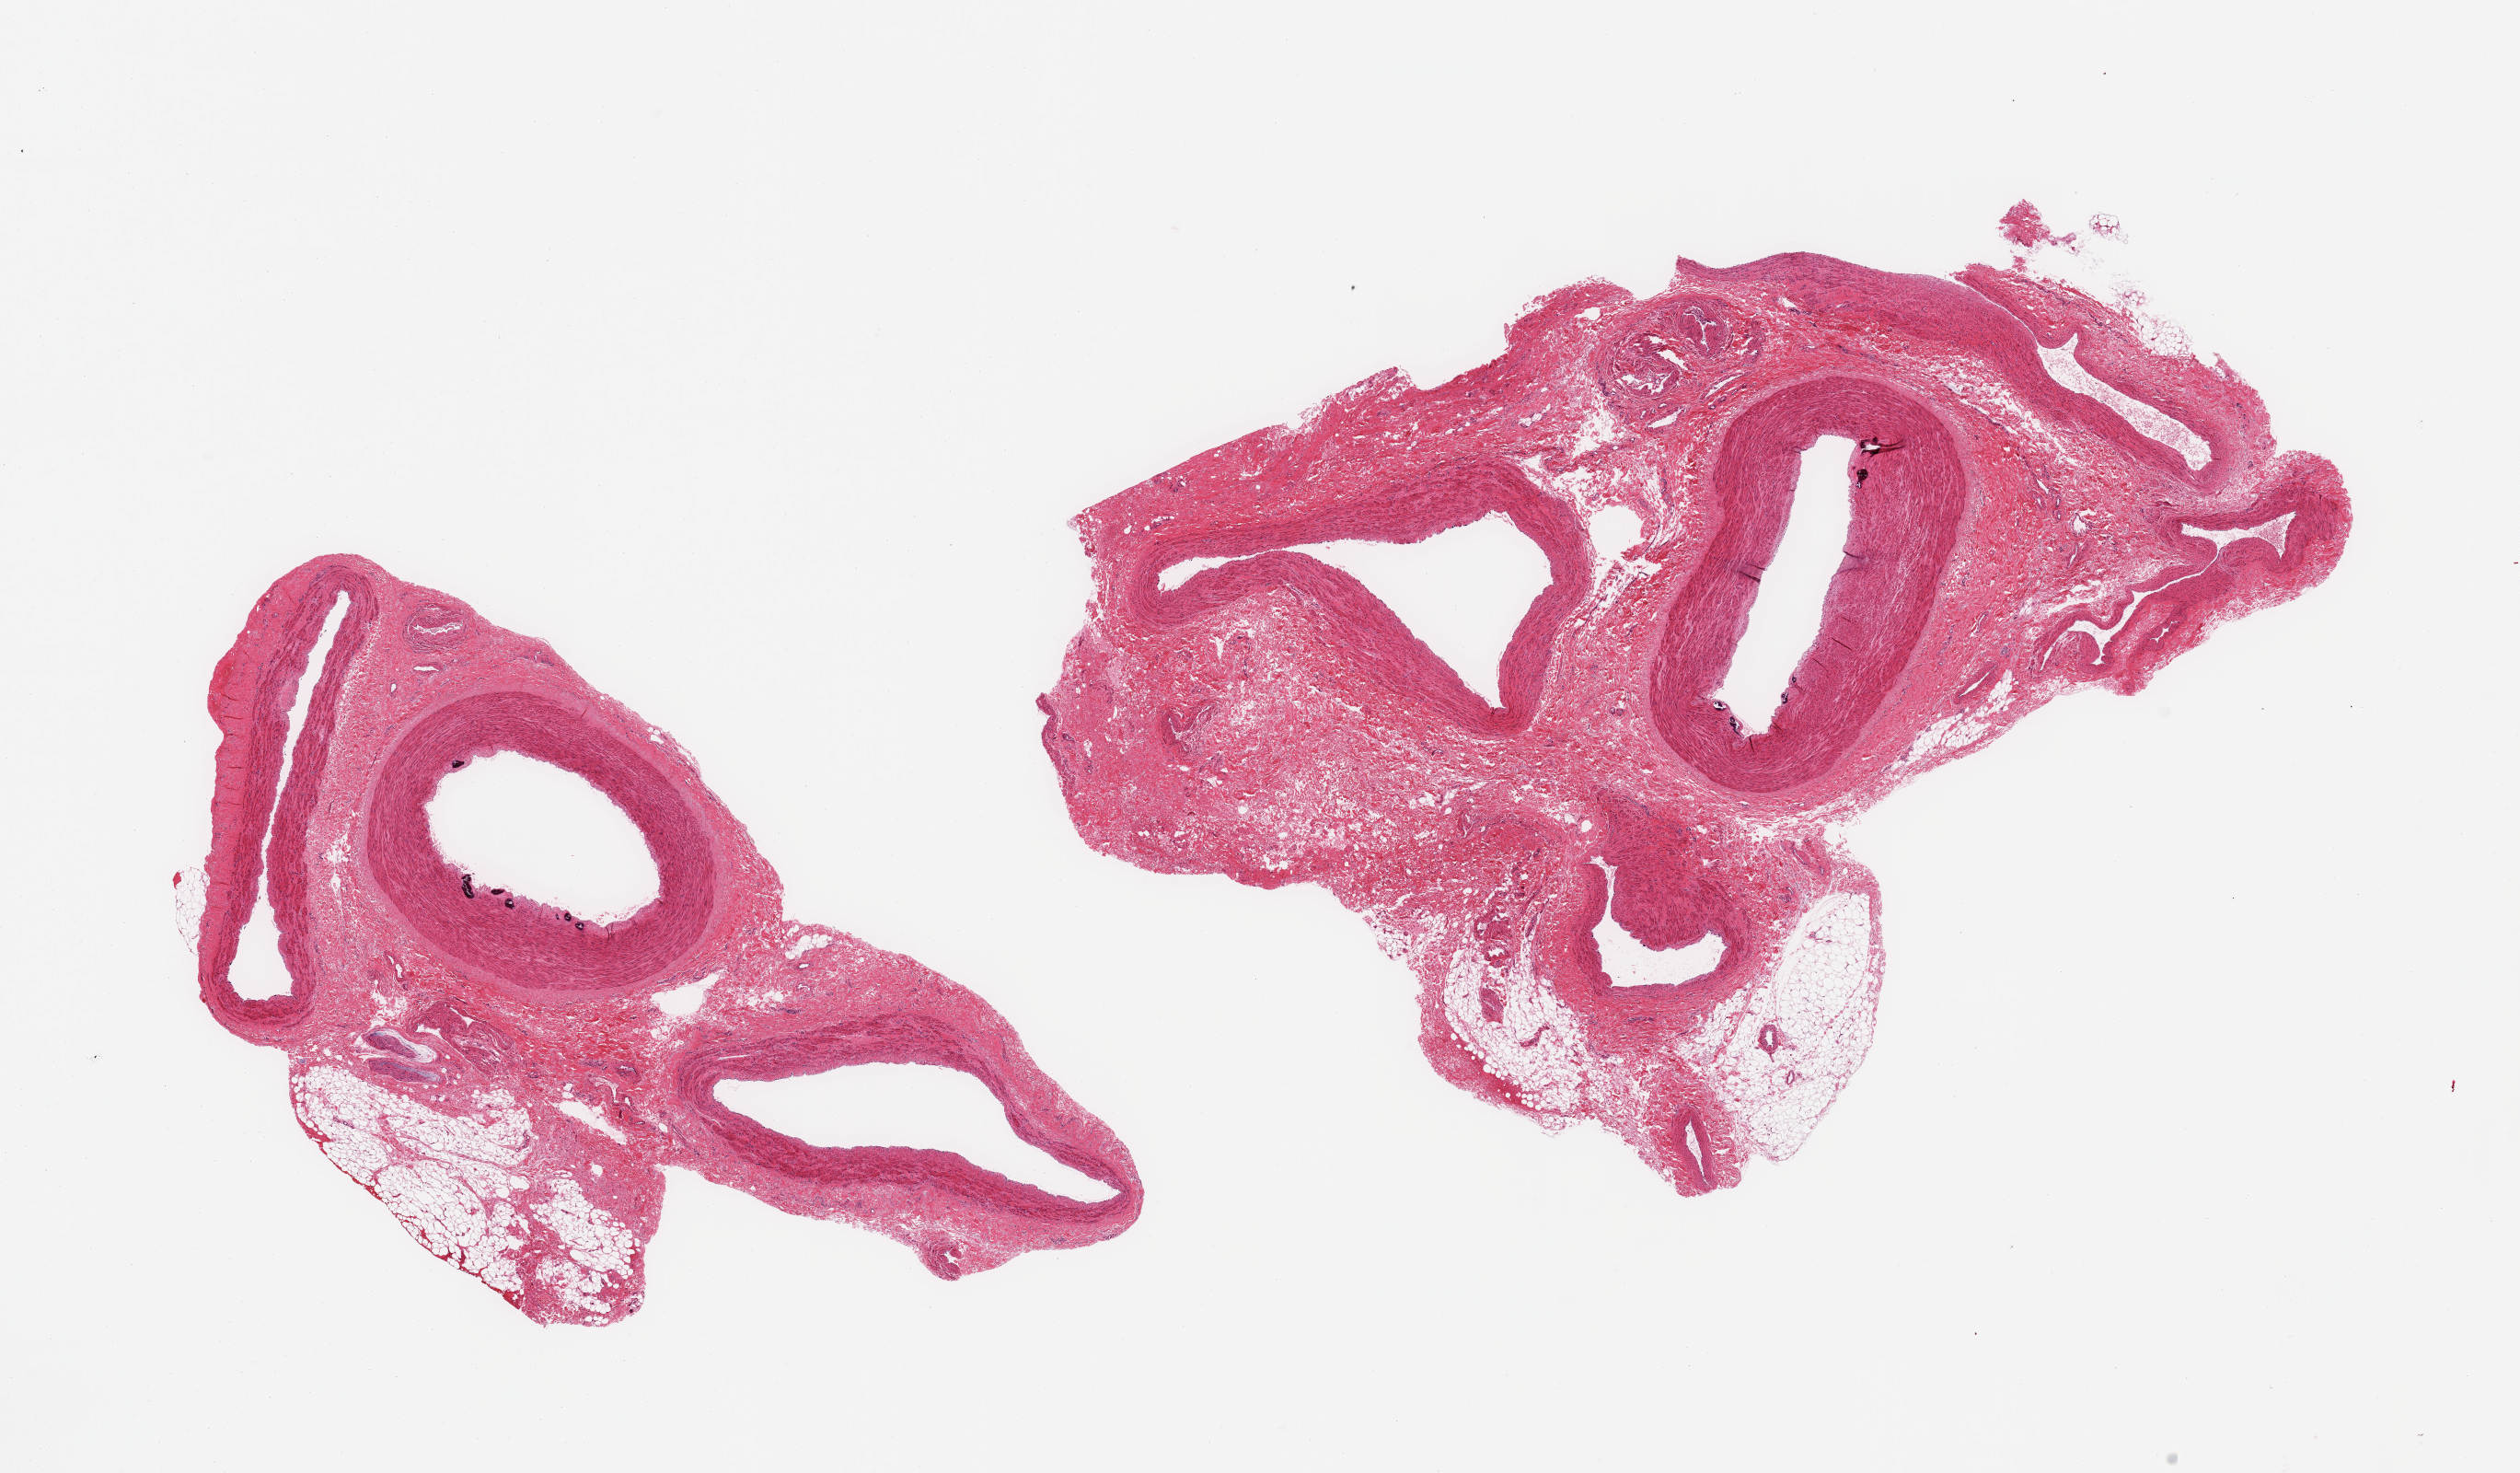
Whole-slide image, hematoxylin and eosin (H&E) stain, brightfield, whole scanned area (about 21.7 x 12.7 mm) shown as a low-resolution overview, PAXgene-fixed paraffin-embedded (PFPE) section, sampled site (target tissue): tibial artery, donor tissue sample. Female donor.
- pathologist's review note for this sample: 2 pieces, ~50% arterial twigs, ~50% fibrous connective & adipose tissue